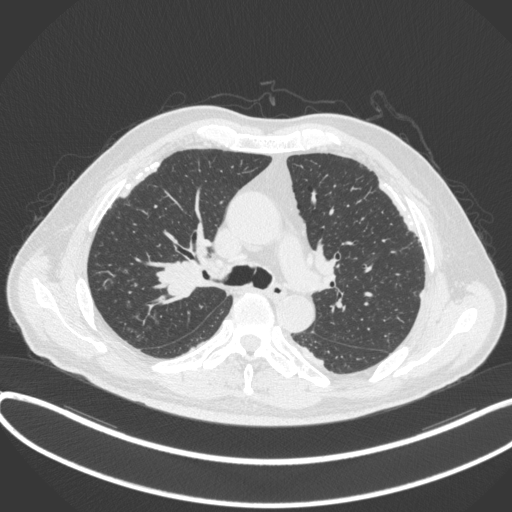
Chest CT, one axial slice; position 278 of 455 along the scan axis; reconstruction kernel B31f; 120 kVp; lung window (W 1500 / L -600 HU); 512 × 512 image matrix, field of view 400 × 400 mm. Male patient, age 58 years. From the clinical record (not read from this slice): clinical TNM (as recorded): T1c N0 M0.
Outlined on this slice (bounding box drawn by a radiologist):
- lung tumour (recorded histology: squamous cell carcinoma): bounding box [x1, y1, x2, y2] px = [148, 257, 212, 307]